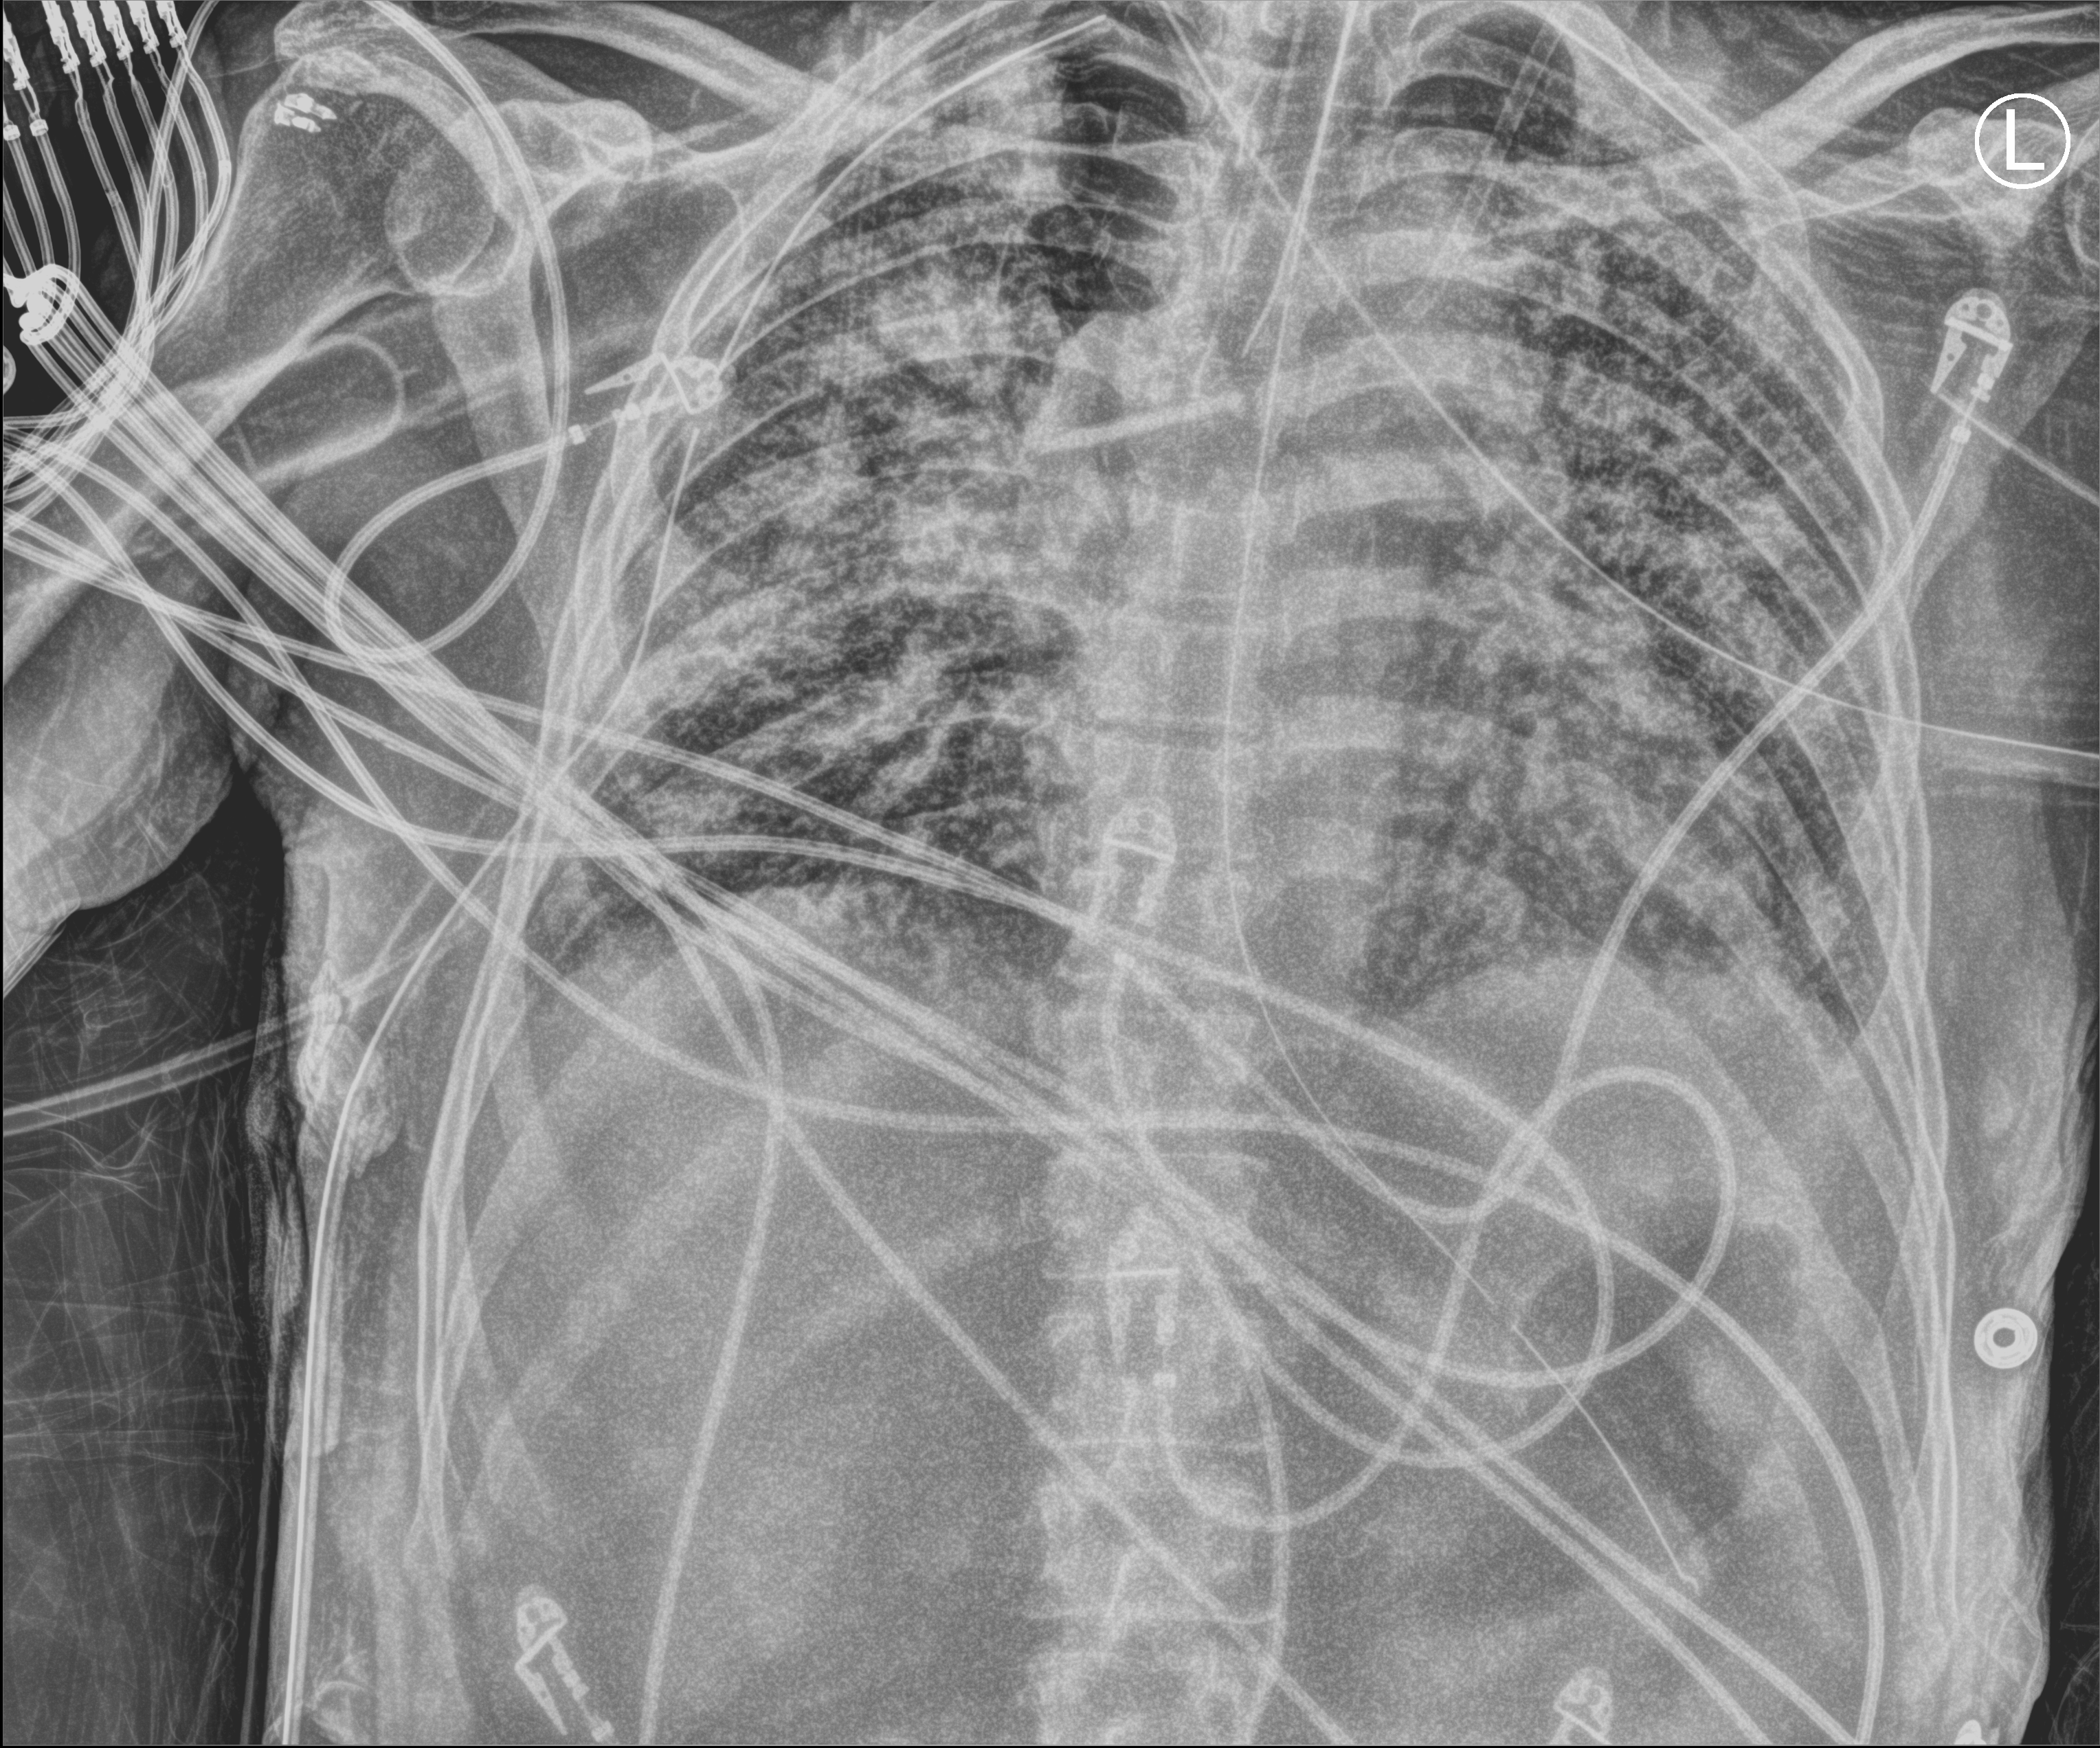
Portable chest radiograph. Patient hospitalised with COVID-19; male, aged 60–74 years.
Admission-level facts for this patient (not findings on this image; timing relative to this image not recorded):
- admitted to intensive care during this hospital stay: yes